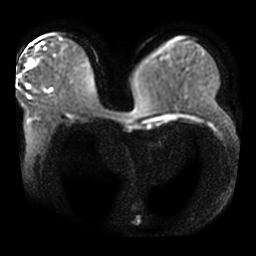
Breast MRI, one axial slice; slice 15 of 42 in the series (ordered by position); diffusion-weighted series; image 2 of 4 stored at this slice position (different b-values; order by instance number); 3 T; 256 × 256 image matrix, field of view 360 × 360 mm. Female patient.
Outlined on this slice (expert manual segmentation):
- tumour on diffusion-weighted imaging: bounding box (x1, y1, x2, y2) in pixels: (28, 63, 32, 67)